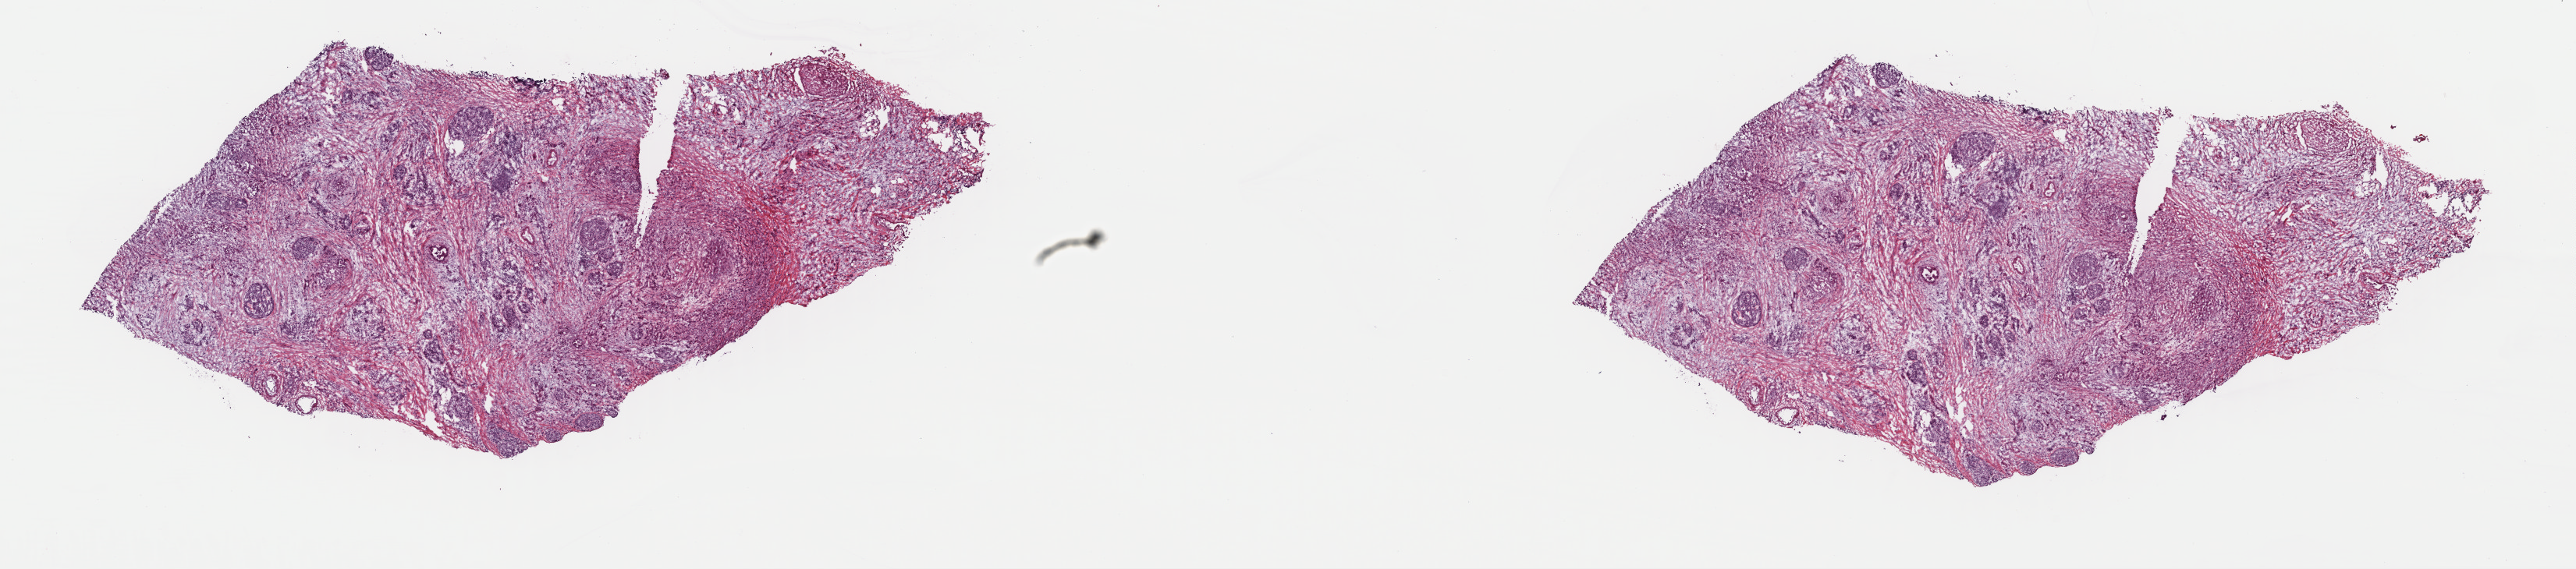
H&E whole-slide image, whole scanned area (about 26.0 x 5.8 mm, from a 40x scan) shown as a low-resolution overview. Frozen section from the top of the tissue portion. Primary tumour sample from the pancreas. Female, age 56 years at initial diagnosis. Histologic grade: G2 (moderately differentiated). Composition of this section per pathologist review: tumour cells 35%, tumour nuclei 70%, normal cells 10%, stromal cells 53%, necrosis 2%. Infiltration values recorded for this section: lymphocyte infiltration 3%, monocyte infiltration 1%, neutrophil infiltration 0%.
* TNM: T2 N0 M0
* AJCC pathologic stage: IB (7th edition)
* lymph nodes positive (case pathology): 0 of 9 examined
* diagnosis: Infiltrating duct carcinoma, NOS